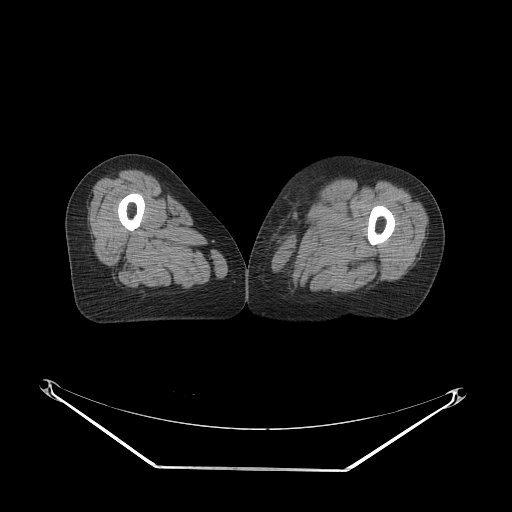
CT of an extremity soft-tissue mass (from a PET/CT study), one axial slice; position 51 of 91 along the scan axis; reconstruction kernel STANDARD; 140 kVp; soft-tissue window (W 400 / L 40 HU); 3.75 mm slice thickness; 512 × 512 image matrix, field of view 500 × 500 mm. Female patient. Case-level facts recorded for this patient, not image findings: histological type: pleomorphic leiomyosarcoma; grade: high; site of the primary tumour: left thigh.
Outlined on this slice (expert contour drawn on MRI and transferred to this co-registered scan by the dataset authors):
- gross tumour volume including surrounding oedema: bounding box <269,199,325,234> (left, top, right, bottom; pixels)